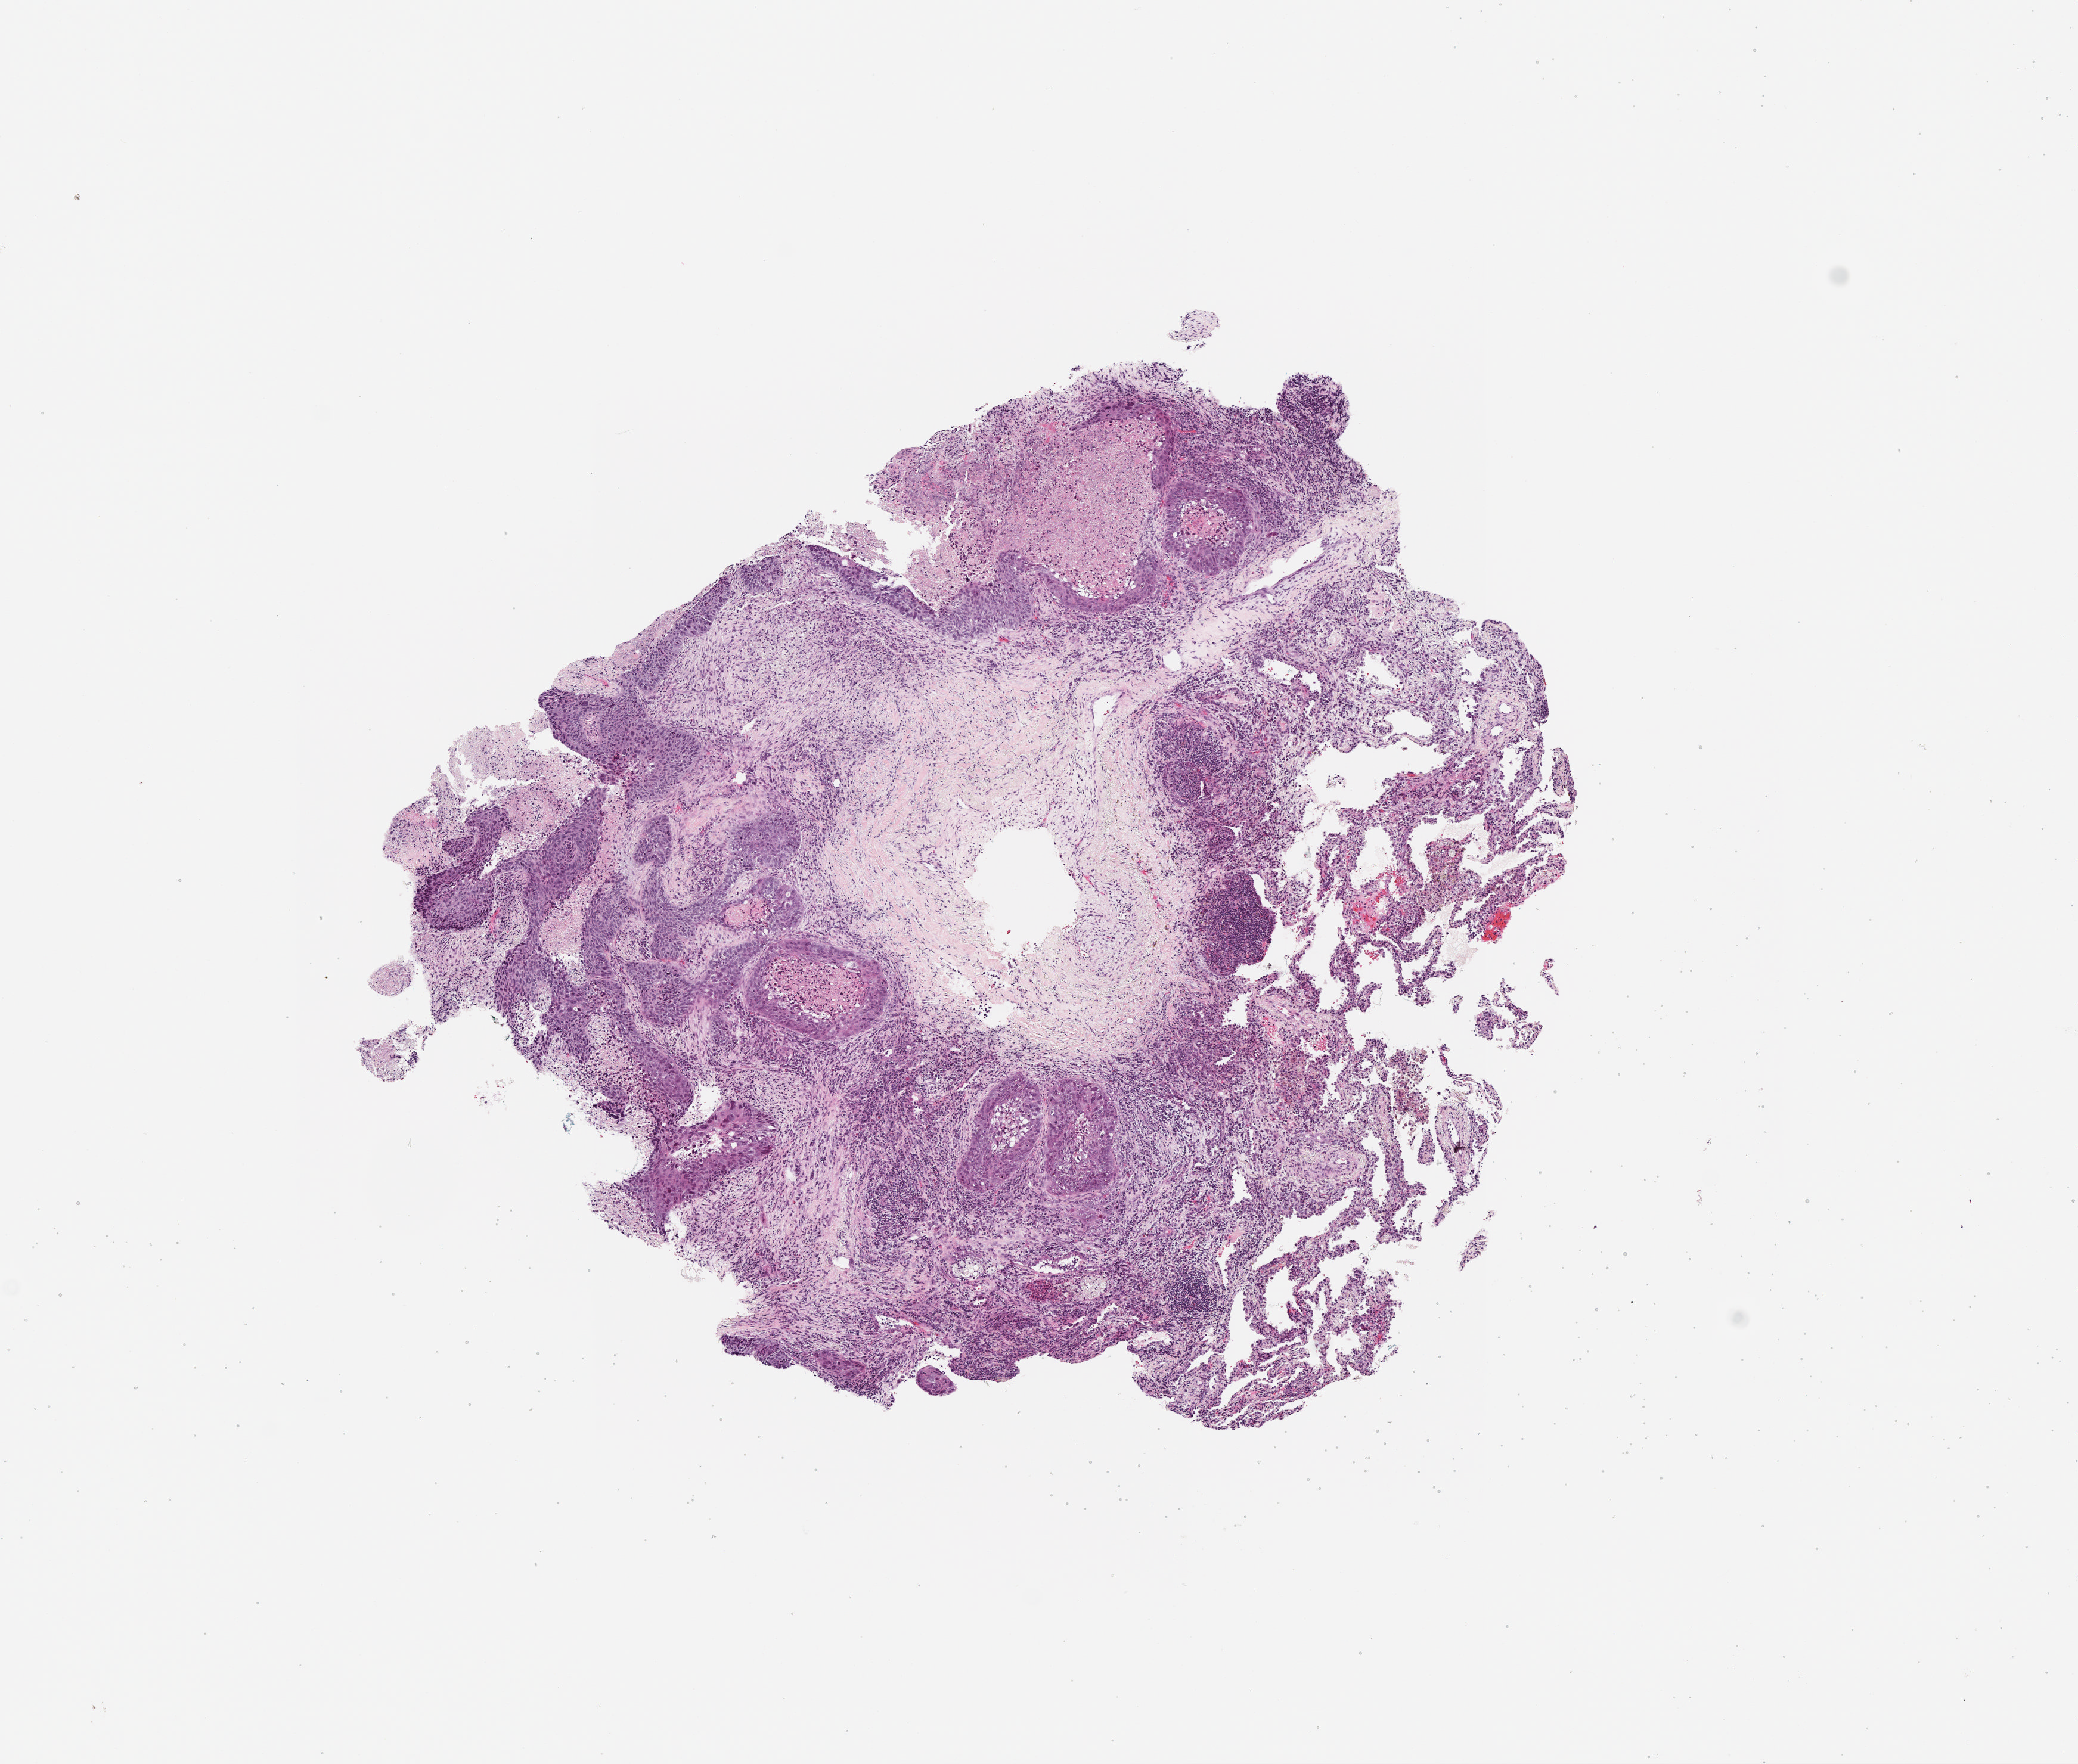
Digitized H&E-stained tissue section (whole slide), whole scanned area (about 7.0 x 6.0 mm, acquisition: 20x scan) shown as a low-resolution overview. Lung, tumour tissue. Patient: male, age 62 years.
Patient diagnosis (cohort enrolment): squamous cell carcinoma (lung).